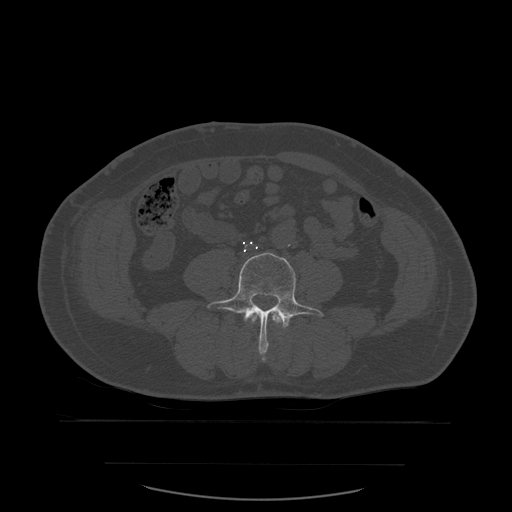
CT including the spine, one axial slice. Slice 169 of 590 in the series (ordered by position). Bone window (W 1800 / L 400 HU). 1.25 mm slice thickness. 512 × 512 image matrix. Patient age 71 years. Case-level facts recorded for this patient, not image findings: primary cancer: lung.
Outlined on this slice (semi-automatically segmented with operator editing):
- L3 vertebra: box from (x=249, y=312) to (x=285, y=327) px
- L4 vertebra: (x=208, y=252)–(x=323, y=360)